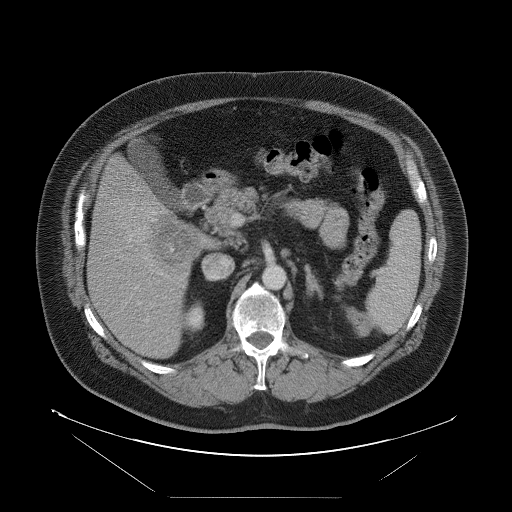
Contrast-enhanced abdominal CT, one axial slice. Slice 48 of 114 in the series (ordered by position). Intravenous contrast given. Soft-tissue window (W 400 / L 40 HU). 5 mm slice thickness. 512 × 512 image matrix. Male patient, age 61 years. Case-level facts recorded for this patient, not image findings: diagnosis: colorectal cancer liver metastases, imaged before liver resection; multiple liver metastases: no; largest metastasis: 6.5 cm; disease in both lobes: yes.
Structures marked on this image (manually delineated by an expert):
- liver: bounding box (x1, y1, x2, y2) in pixels: (89, 157, 214, 358)
- liver metastasis: (154, 214, 205, 267)